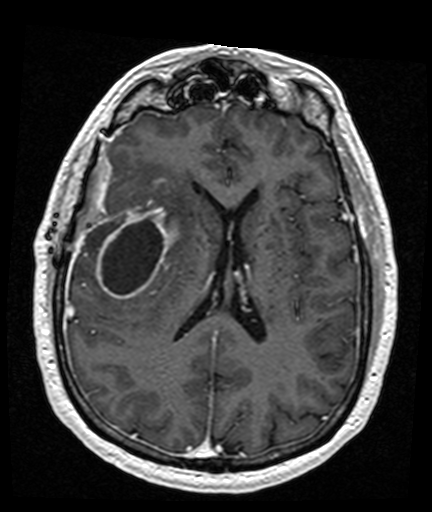
Brain MRI from a brain-tumour surgery series, one axial slice; slice 71 of 176 in the series (ordered by position); T1-weighted post-contrast; 1 mm slice thickness; 432 × 512 image matrix, field of view 194 × 230 mm. From the clinical record (not read from this slice): histopathology: Glioblastoma; WHO grade: 4; IDH mutation: no; tumour location: Right Frontal Temporal, Posterior Sylvian Fissure.
Outlined on this slice (outlined manually by an expert reader):
- tumour: bounding box <96,180,172,300> (left, top, right, bottom; pixels)